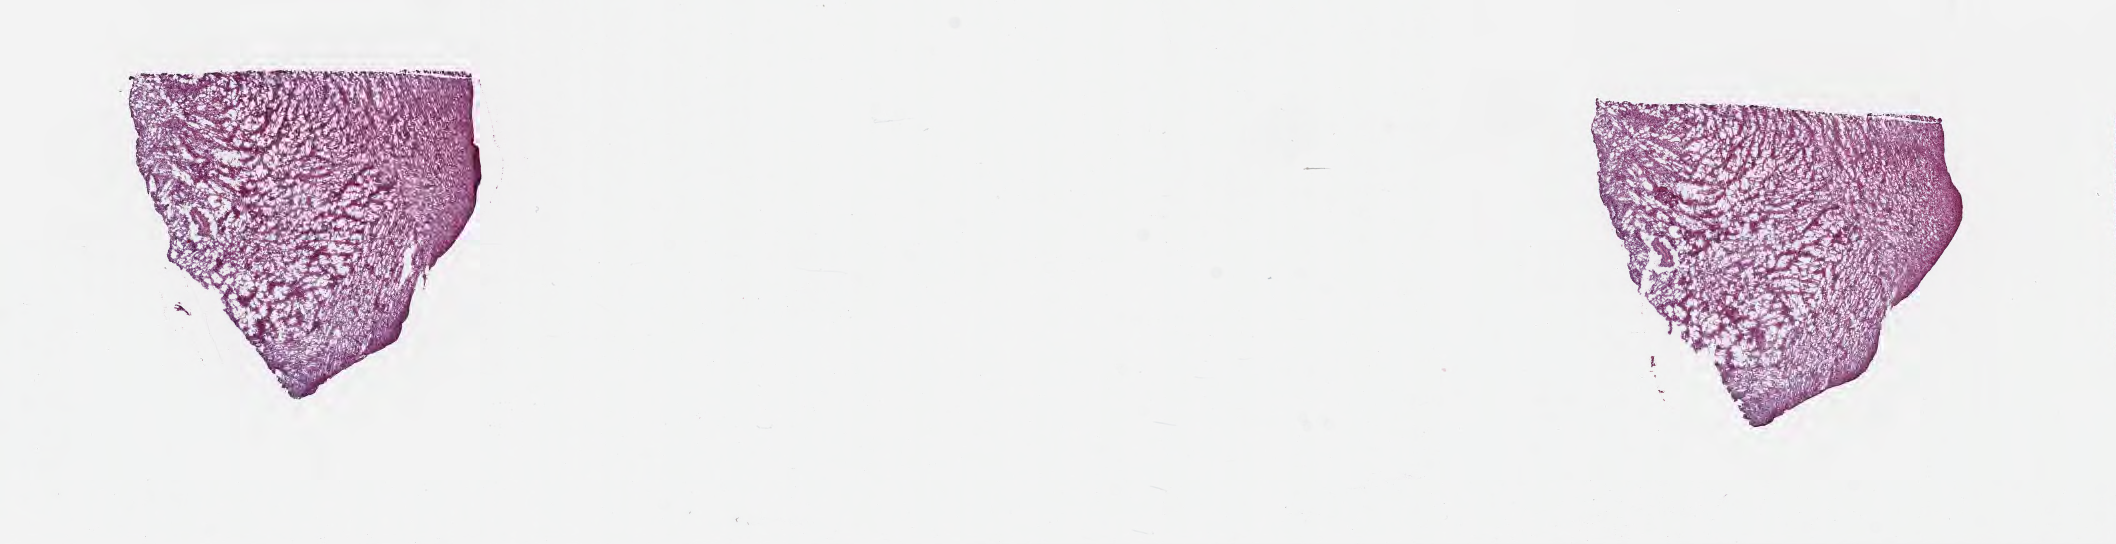
Digitized hematoxylin and eosin (H&E)-stained section — low-resolution overview of the scanned area, about 17.1 x 4.4 mm, cryosection, specimen: primary tumor, anatomic site: brain. Patient: female, age at initial diagnosis 63 years. Slide review estimates, as recorded: tumor cells 88%, tumor nuclei 95%, stromal cells 7%, necrosis 0%, normal cells 5%. Inflammatory infiltration, as recorded: lymphocyte infiltration 0%, monocyte infiltration 0%, neutrophil infiltration 0%.
- histologic diagnosis: Glioblastoma, NOS